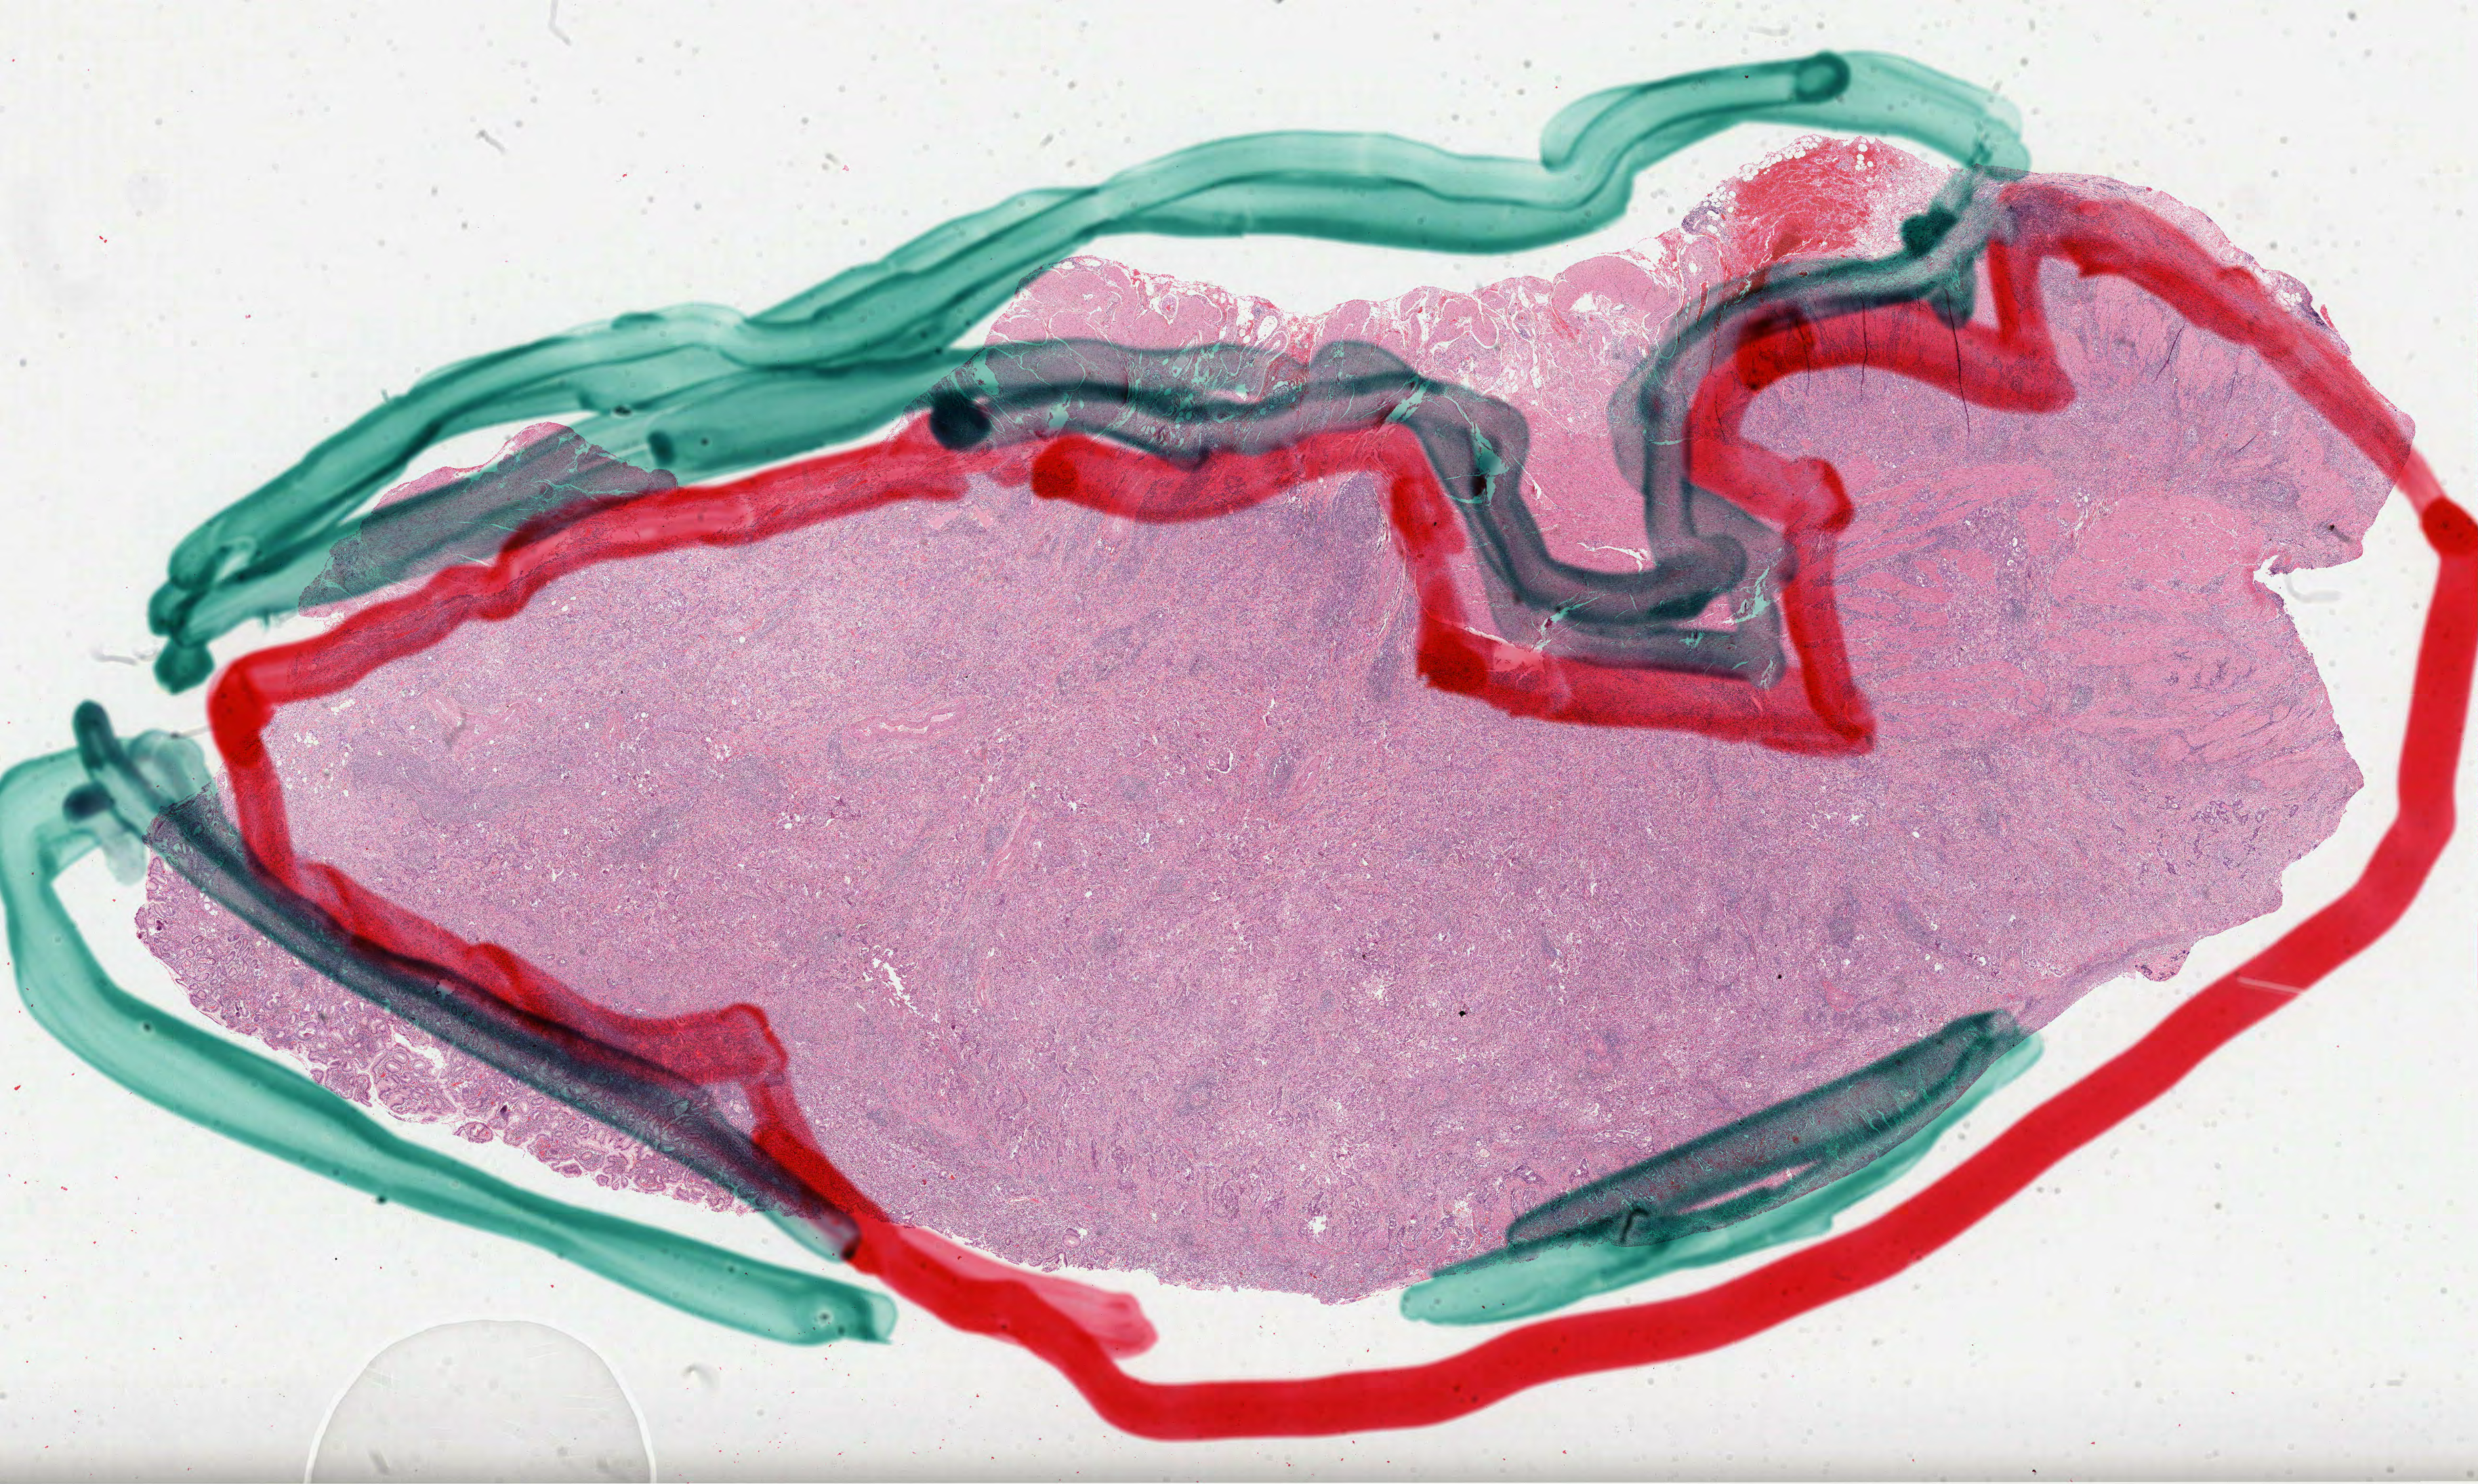
Digitized H&E-stained tissue section (whole slide), shown as a low-resolution overview of the whole scanned area (about 29.5 x 17.7 mm, acquisition: 40x scan); formalin-fixed paraffin-embedded (FFPE) diagnostic section; primary tumour sample from the stomach. Female patient; age at initial diagnosis 62 years. Histologic grade: G2 (moderately differentiated).
* lymph nodes positive (case pathology): 1 of 4 examined
* pathologic diagnosis: Adenocarcinoma, NOS (body of stomach)
* AJCC pathologic stage: IIB (7th edition)